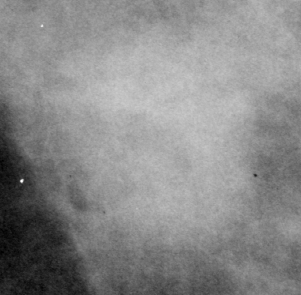
Cropped region of a digitized screen-film mammogram centred on a radiologist-marked abnormality; left breast; CC view; BI-RADS breast density category 3 (scale 1–4).
- Finding: mass, shape irregular, margins obscured / ill defined; BI-RADS assessment category 3; subtlety rating 3 on a 1 (subtle) to 5 (obvious) scale; pathology (as recorded): malignant.